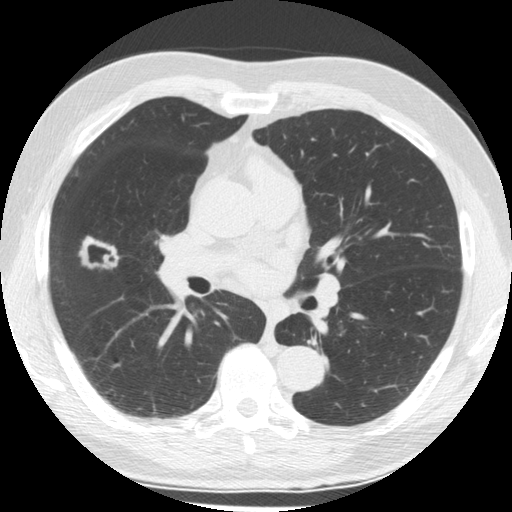
Axial slice from a low-dose chest CT screening exam, baseline screening round, lung window (W 1500 / L -600 HU), 2.5 mm slice thickness, standard (soft-tissue) reconstruction kernel (STANDARD), 120 kVp, 512 × 512 image matrix. Male participant, aged 64 years at enrolment.
Expert-annotated lung lesion, box from (x=68, y=221) to (x=129, y=284) px. The screening reader recorded 2 non-calcified nodules or masses ≥4 mm on this exam (right middle lobe, left lower lobe); which of them this box marks is not recorded. Later outcome: lung cancer diagnosed 58 days after this screen — papillary adenocarcinoma, NOS, right middle lobe, well differentiated (G1), stage IA (AJCC 6th edition), 25 mm at pathology.